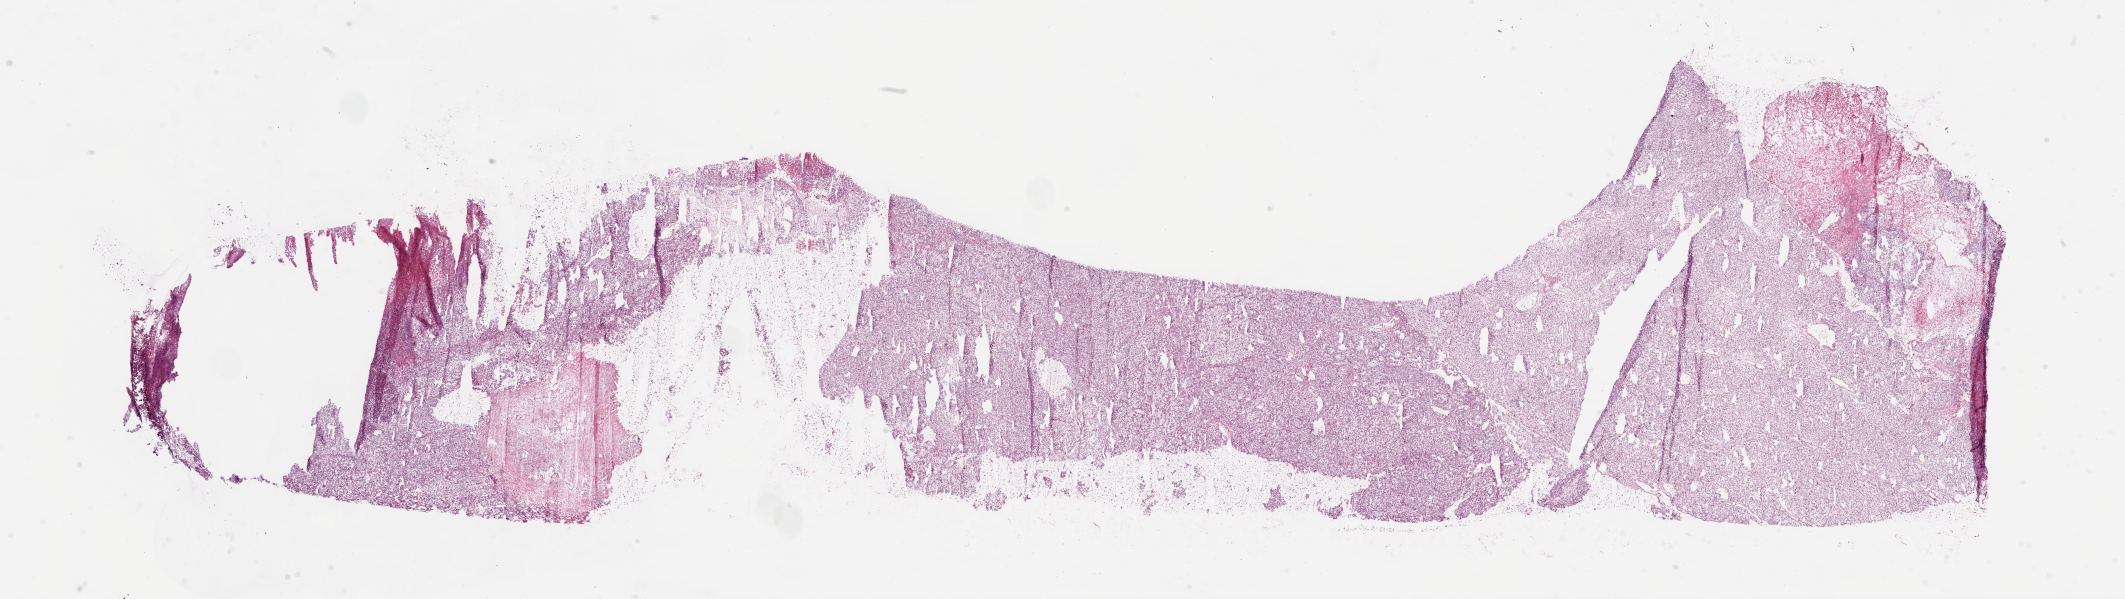
H&E whole-slide image — low-resolution overview of the scanned area, about 34.1 x 9.6 mm, frozen section from the bottom of the tissue portion, sample: primary tumour, kidney. Male, age 63 years at initial diagnosis. Histologic grade: G4 (undifferentiated). Pathologist review of this section (percent, as recorded): tumour cells 83%, tumour nuclei 85%, normal cells 0%, stromal cells 15%, necrosis 2%.
Laterality: left. TNM: T3a NX M1. AJCC pathologic stage: IV. Pathologic diagnosis: Clear cell adenocarcinoma, NOS.